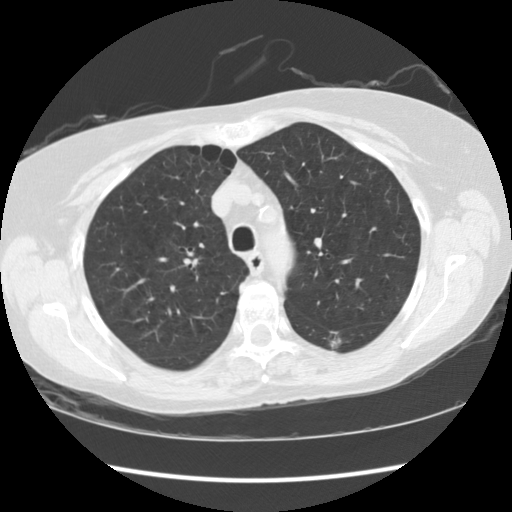
Chest CT (low-dose screening protocol), one axial image; third annual screen; lung window (W 1500 / L -600 HU); 2.5 mm slice thickness; slice 31 of 119 in the series; 512 × 512 image matrix. Female participant, aged 63 years at enrolment.
Lesion marked by an expert reader, box from (x=308, y=322) to (x=360, y=361) px. The screening reader recorded 4 non-calcified nodules or masses ≥4 mm on this exam (left lower lobe, right upper lobe, left upper lobe, left lower lobe); which of them this box marks is not recorded. Official screen result: positive, other. Lung cancer was diagnosed 60 days after this screen: squamous cell carcinoma, NOS, left lower lobe, moderately differentiated (G2), stage IB (AJCC 6th edition), 15 mm at pathology.